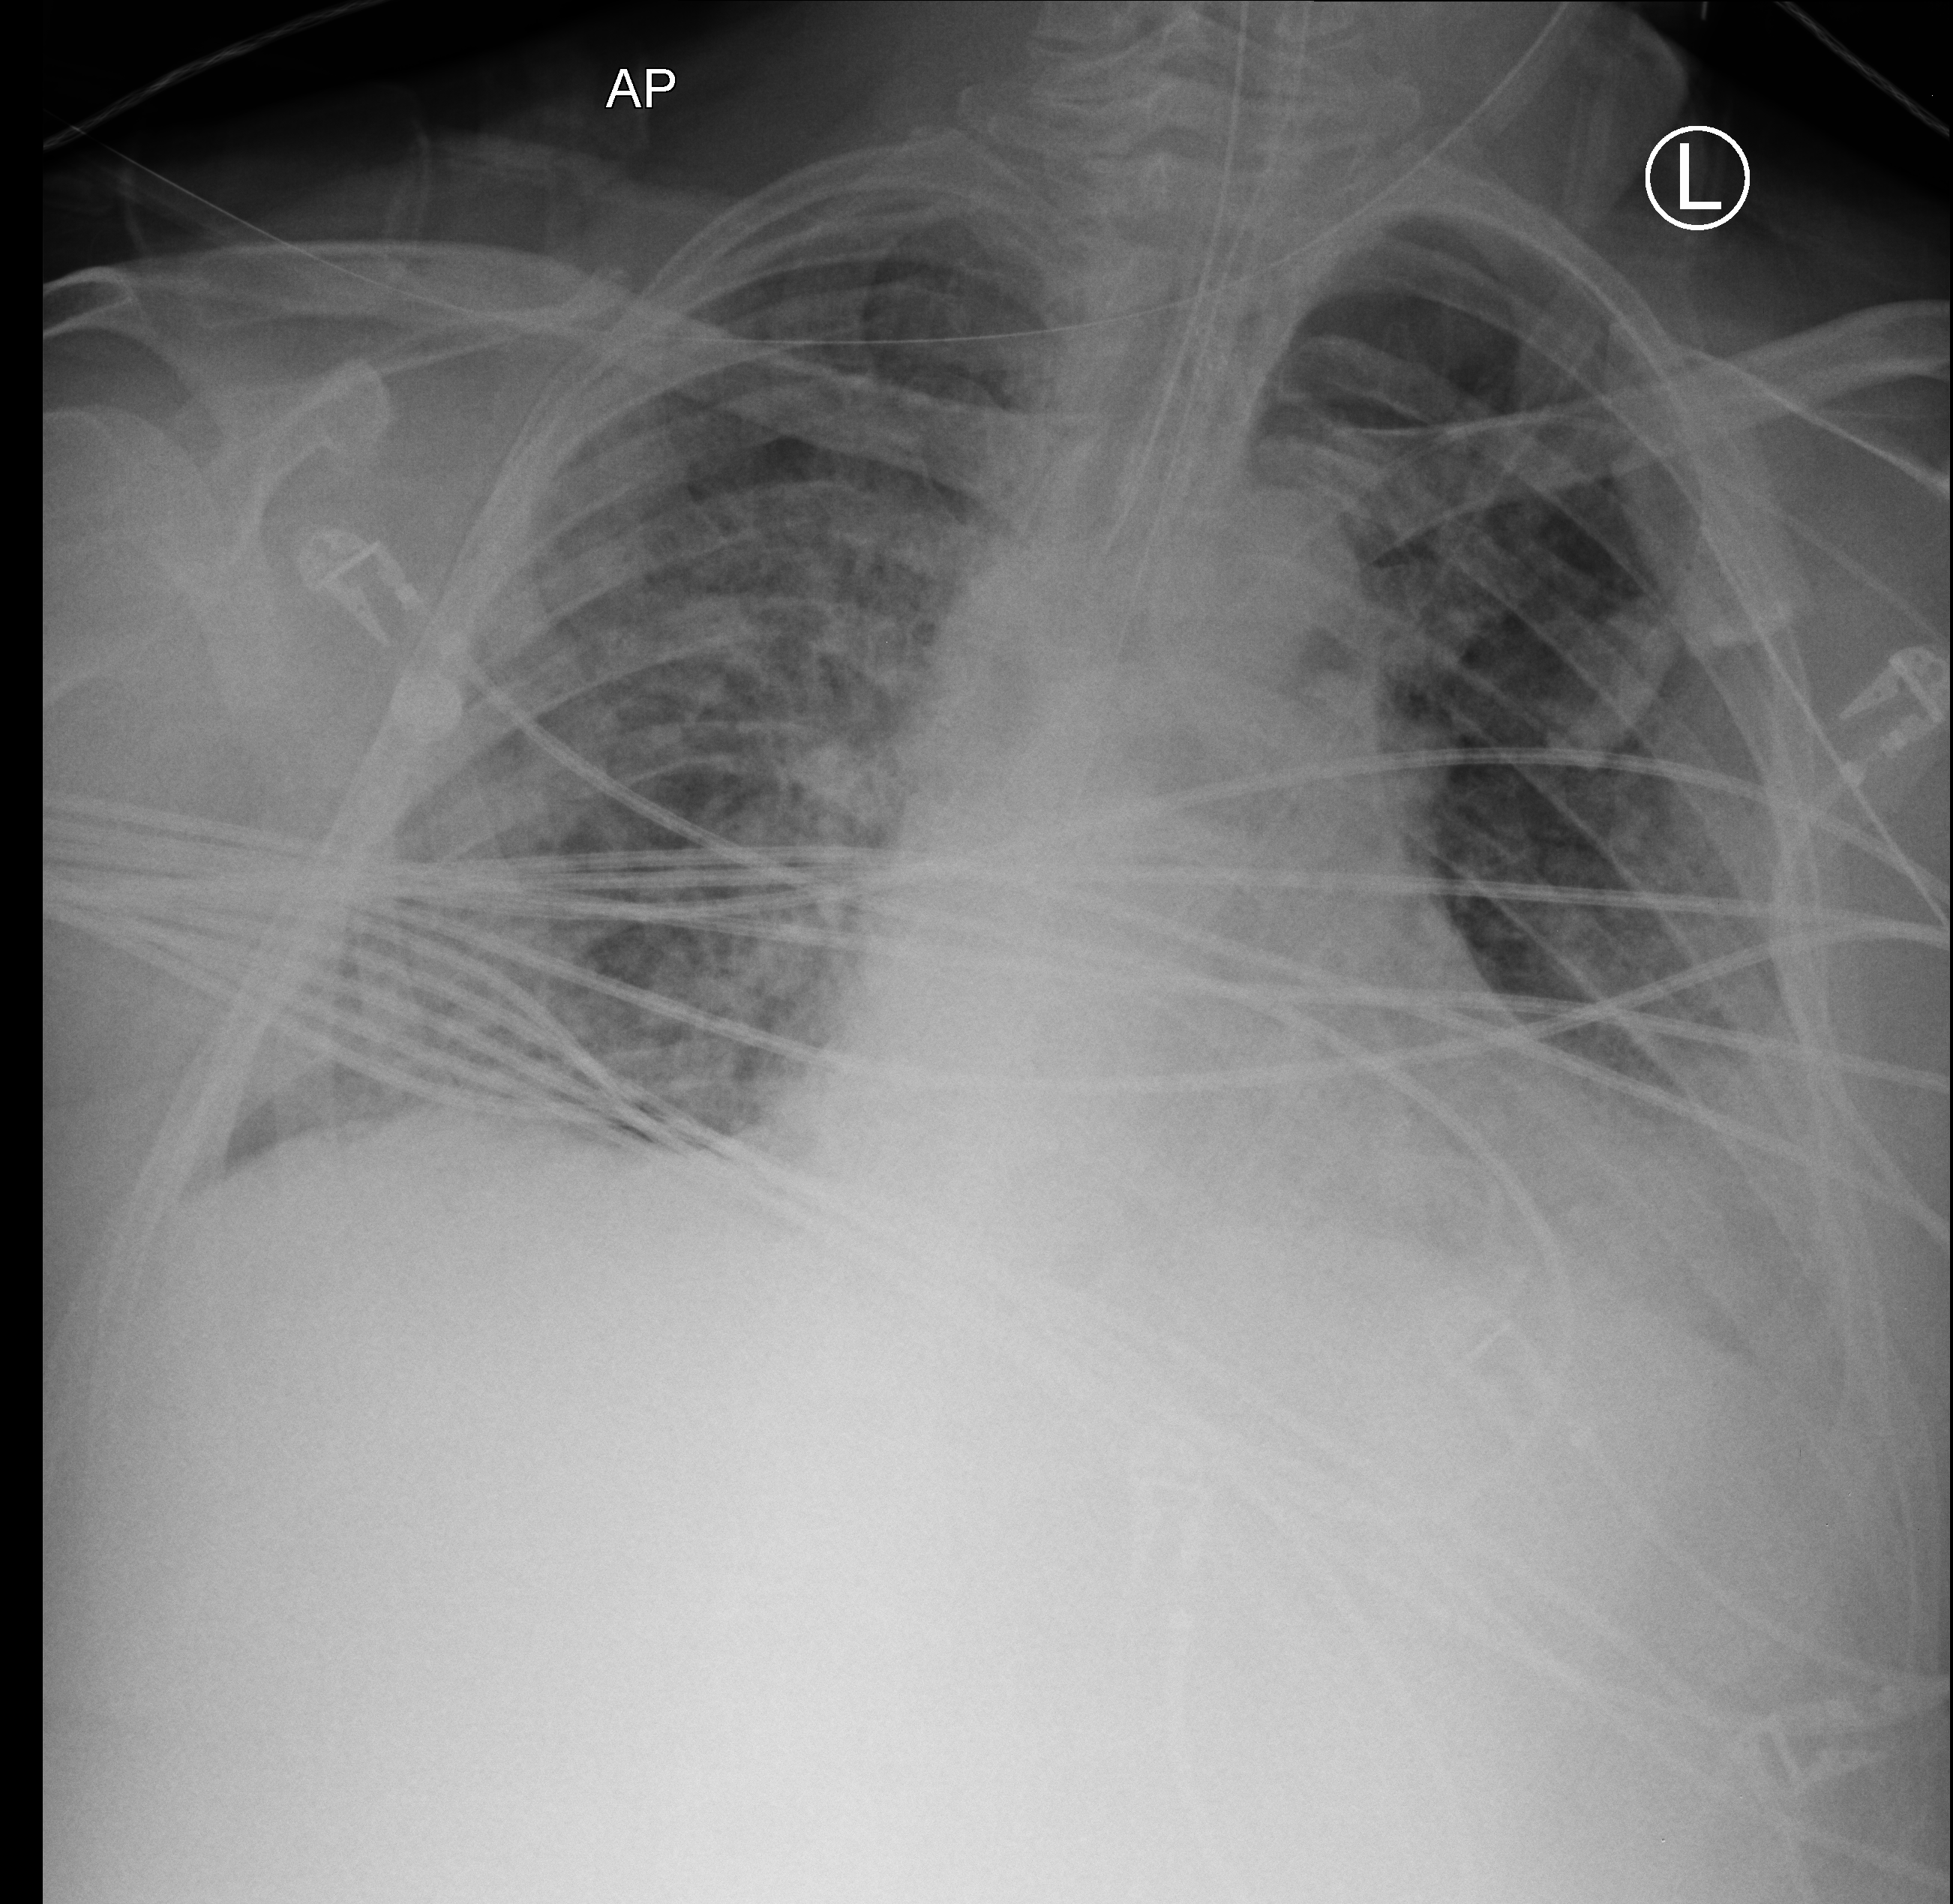
Bedside chest radiograph (computed radiography). Patient hospitalised with COVID-19; male, aged 18–59 years.
Admission-level facts for this patient (not findings on this image; timing relative to this image not recorded): chronic kidney disease (admission record): no.